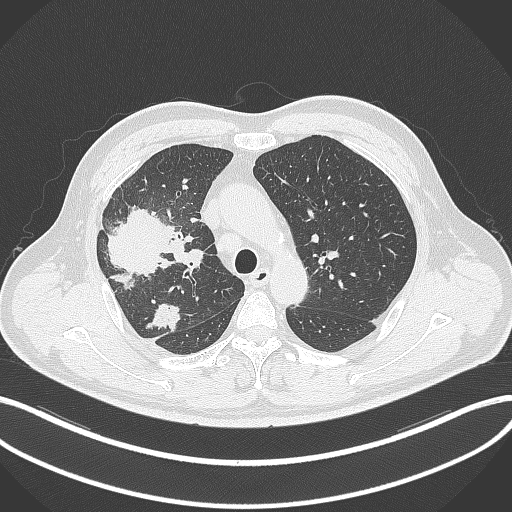
Chest CT, one axial slice. Slice 236 of 348 in the series (ordered by position). Reconstruction kernel B70f. 120 kVp. Lung window (W 1500 / L -600 HU). 1 mm slice thickness. 512 × 512 image matrix. Patient: male, 55 years. Case-level facts recorded for this patient, not image findings: clinical TNM (as recorded): T3 N2 M1.
Annotated regions visible in this slice (bounding box drawn by a radiologist):
- lung tumour (recorded histology: adenocarcinoma): bounding box [x1, y1, x2, y2] px = [99, 204, 168, 292]